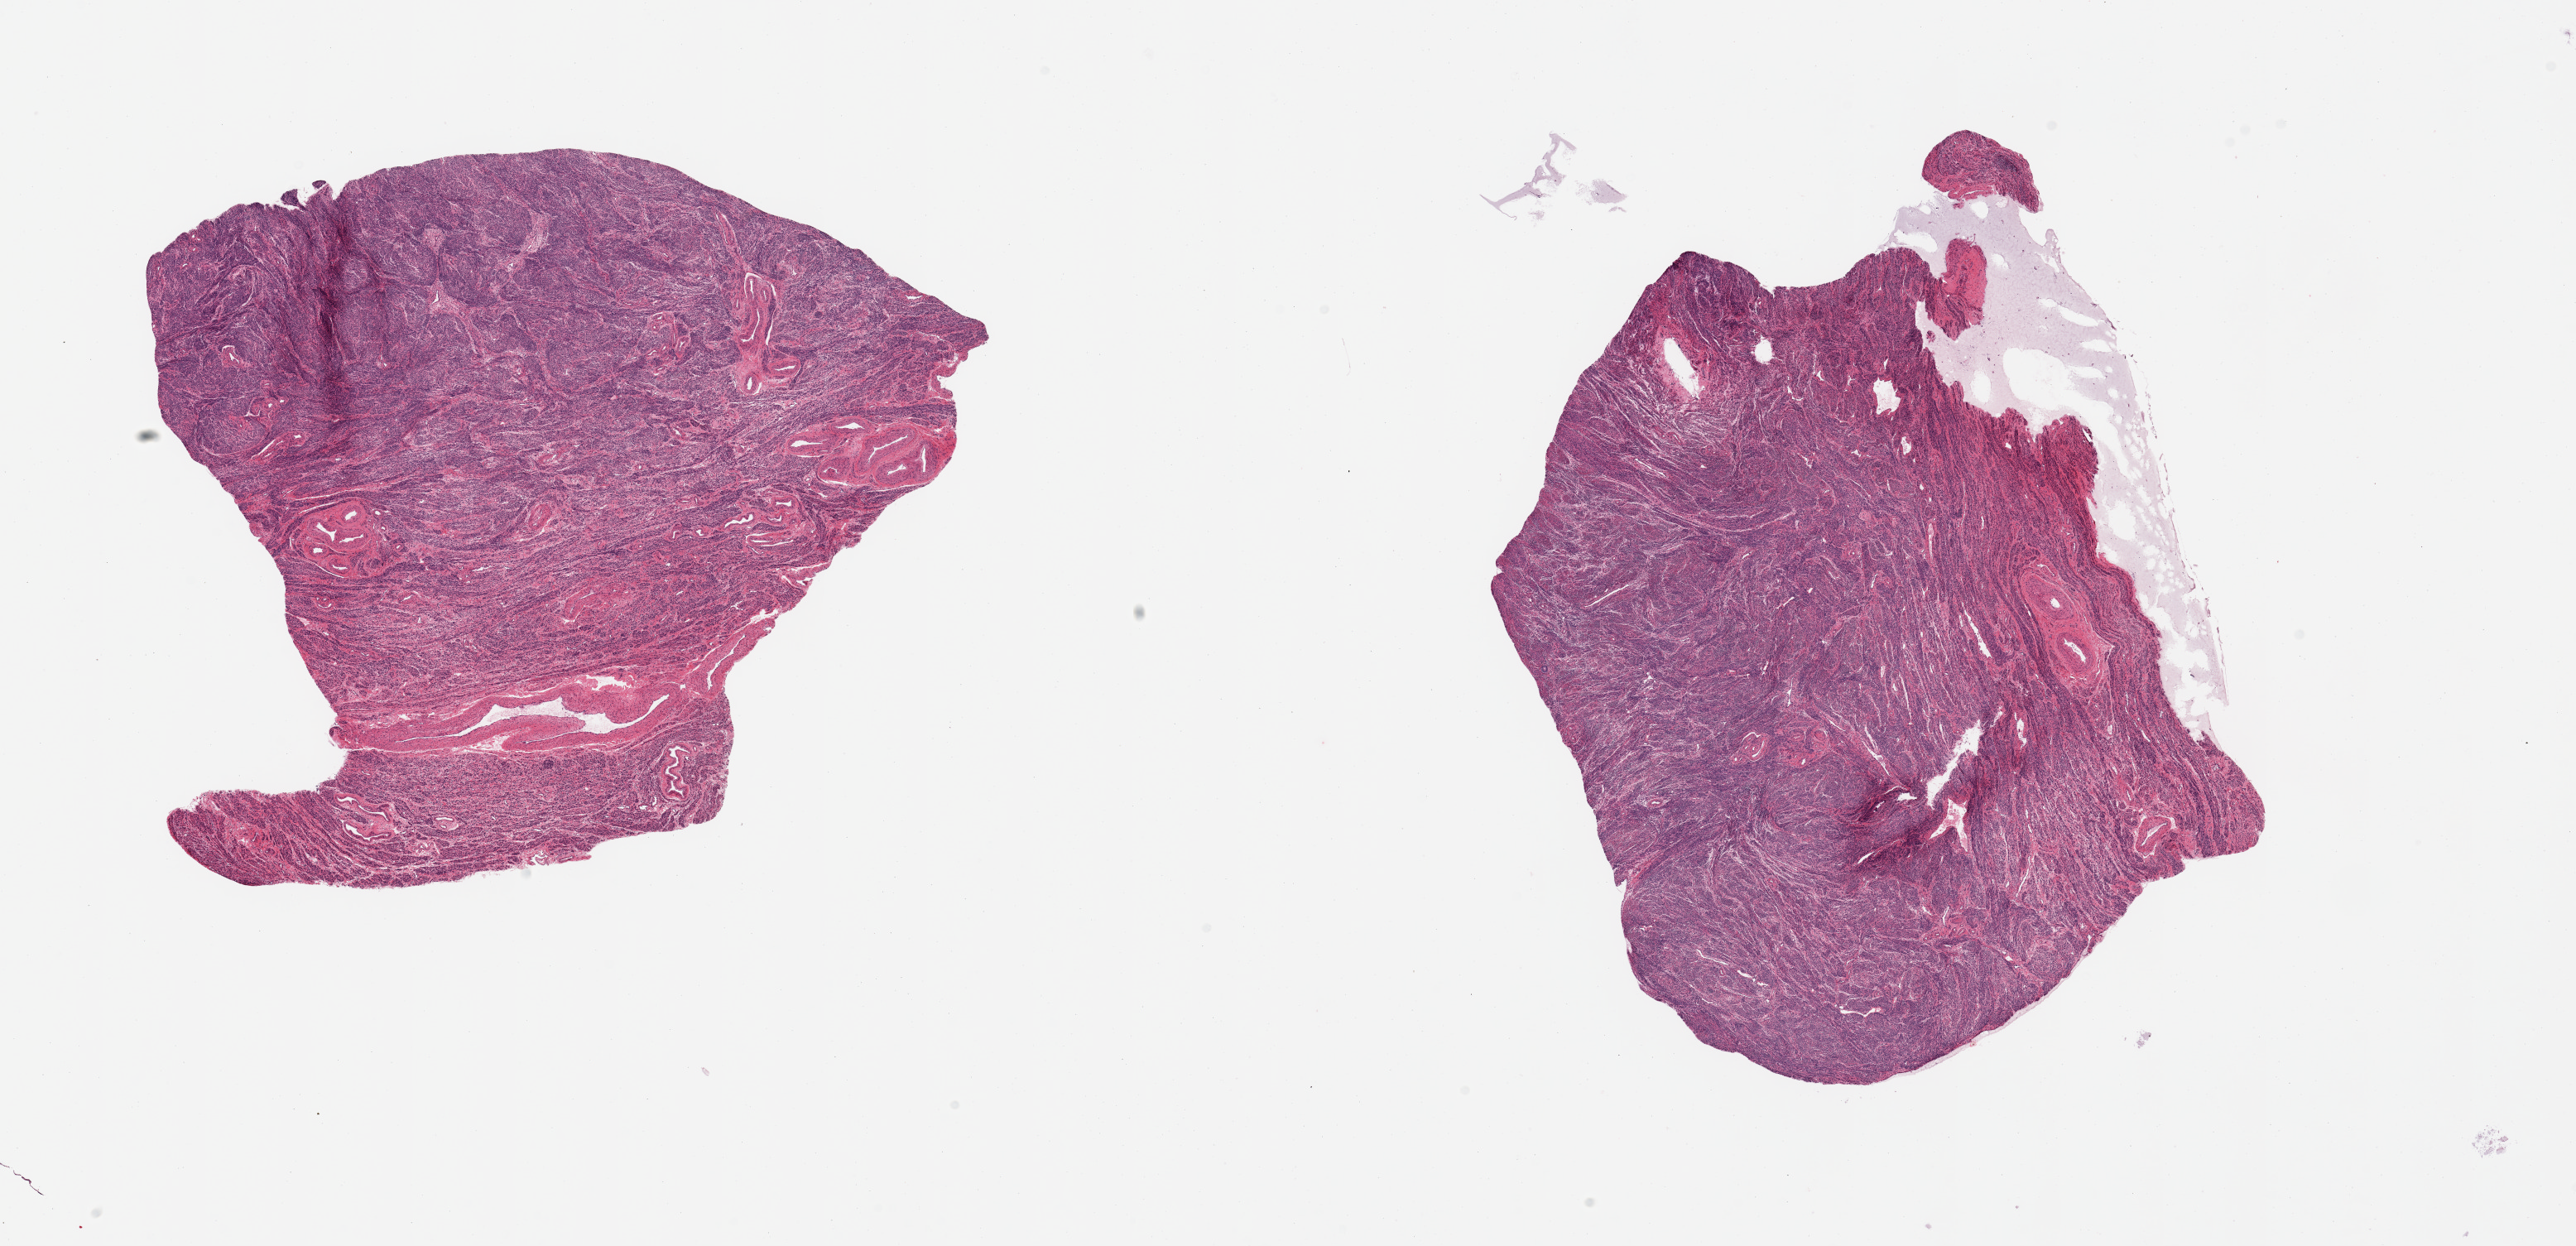
Whole-slide image, haematoxylin and eosin stain — a low-resolution overview of the entire scanned area, about 24.6 x 11.9 mm (acquisition: 20x scan); PAXgene-fixed paraffin-embedded (PFPE) section; section of uterus (target tissue); donor tissue sample. Donor: female.
* pathologist's review note for this sample: 2 pieces, all myometrium